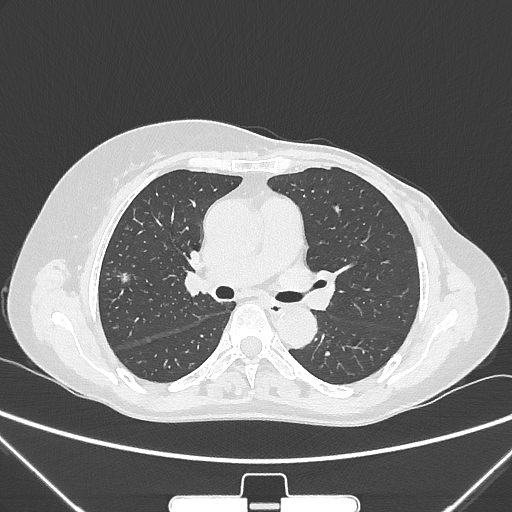
Chest CT, one axial slice. Slice 151 of 265 in the series (ordered by position). 120 kVp. Lung window (W 1500 / L -600 HU). 1 mm slice thickness. 512 × 512 image matrix, field of view 350 × 350 mm. Patient: female, 64 years. From the clinical record (not read from this slice): clinical TNM (as recorded): T1c N0 M0; histopathological grade: G1-2.
Structures marked on this image (rectangle marked by the reading radiologist):
- lung tumour (recorded histology: adenocarcinoma): bounding box [x1, y1, x2, y2] px = [110, 263, 134, 290]